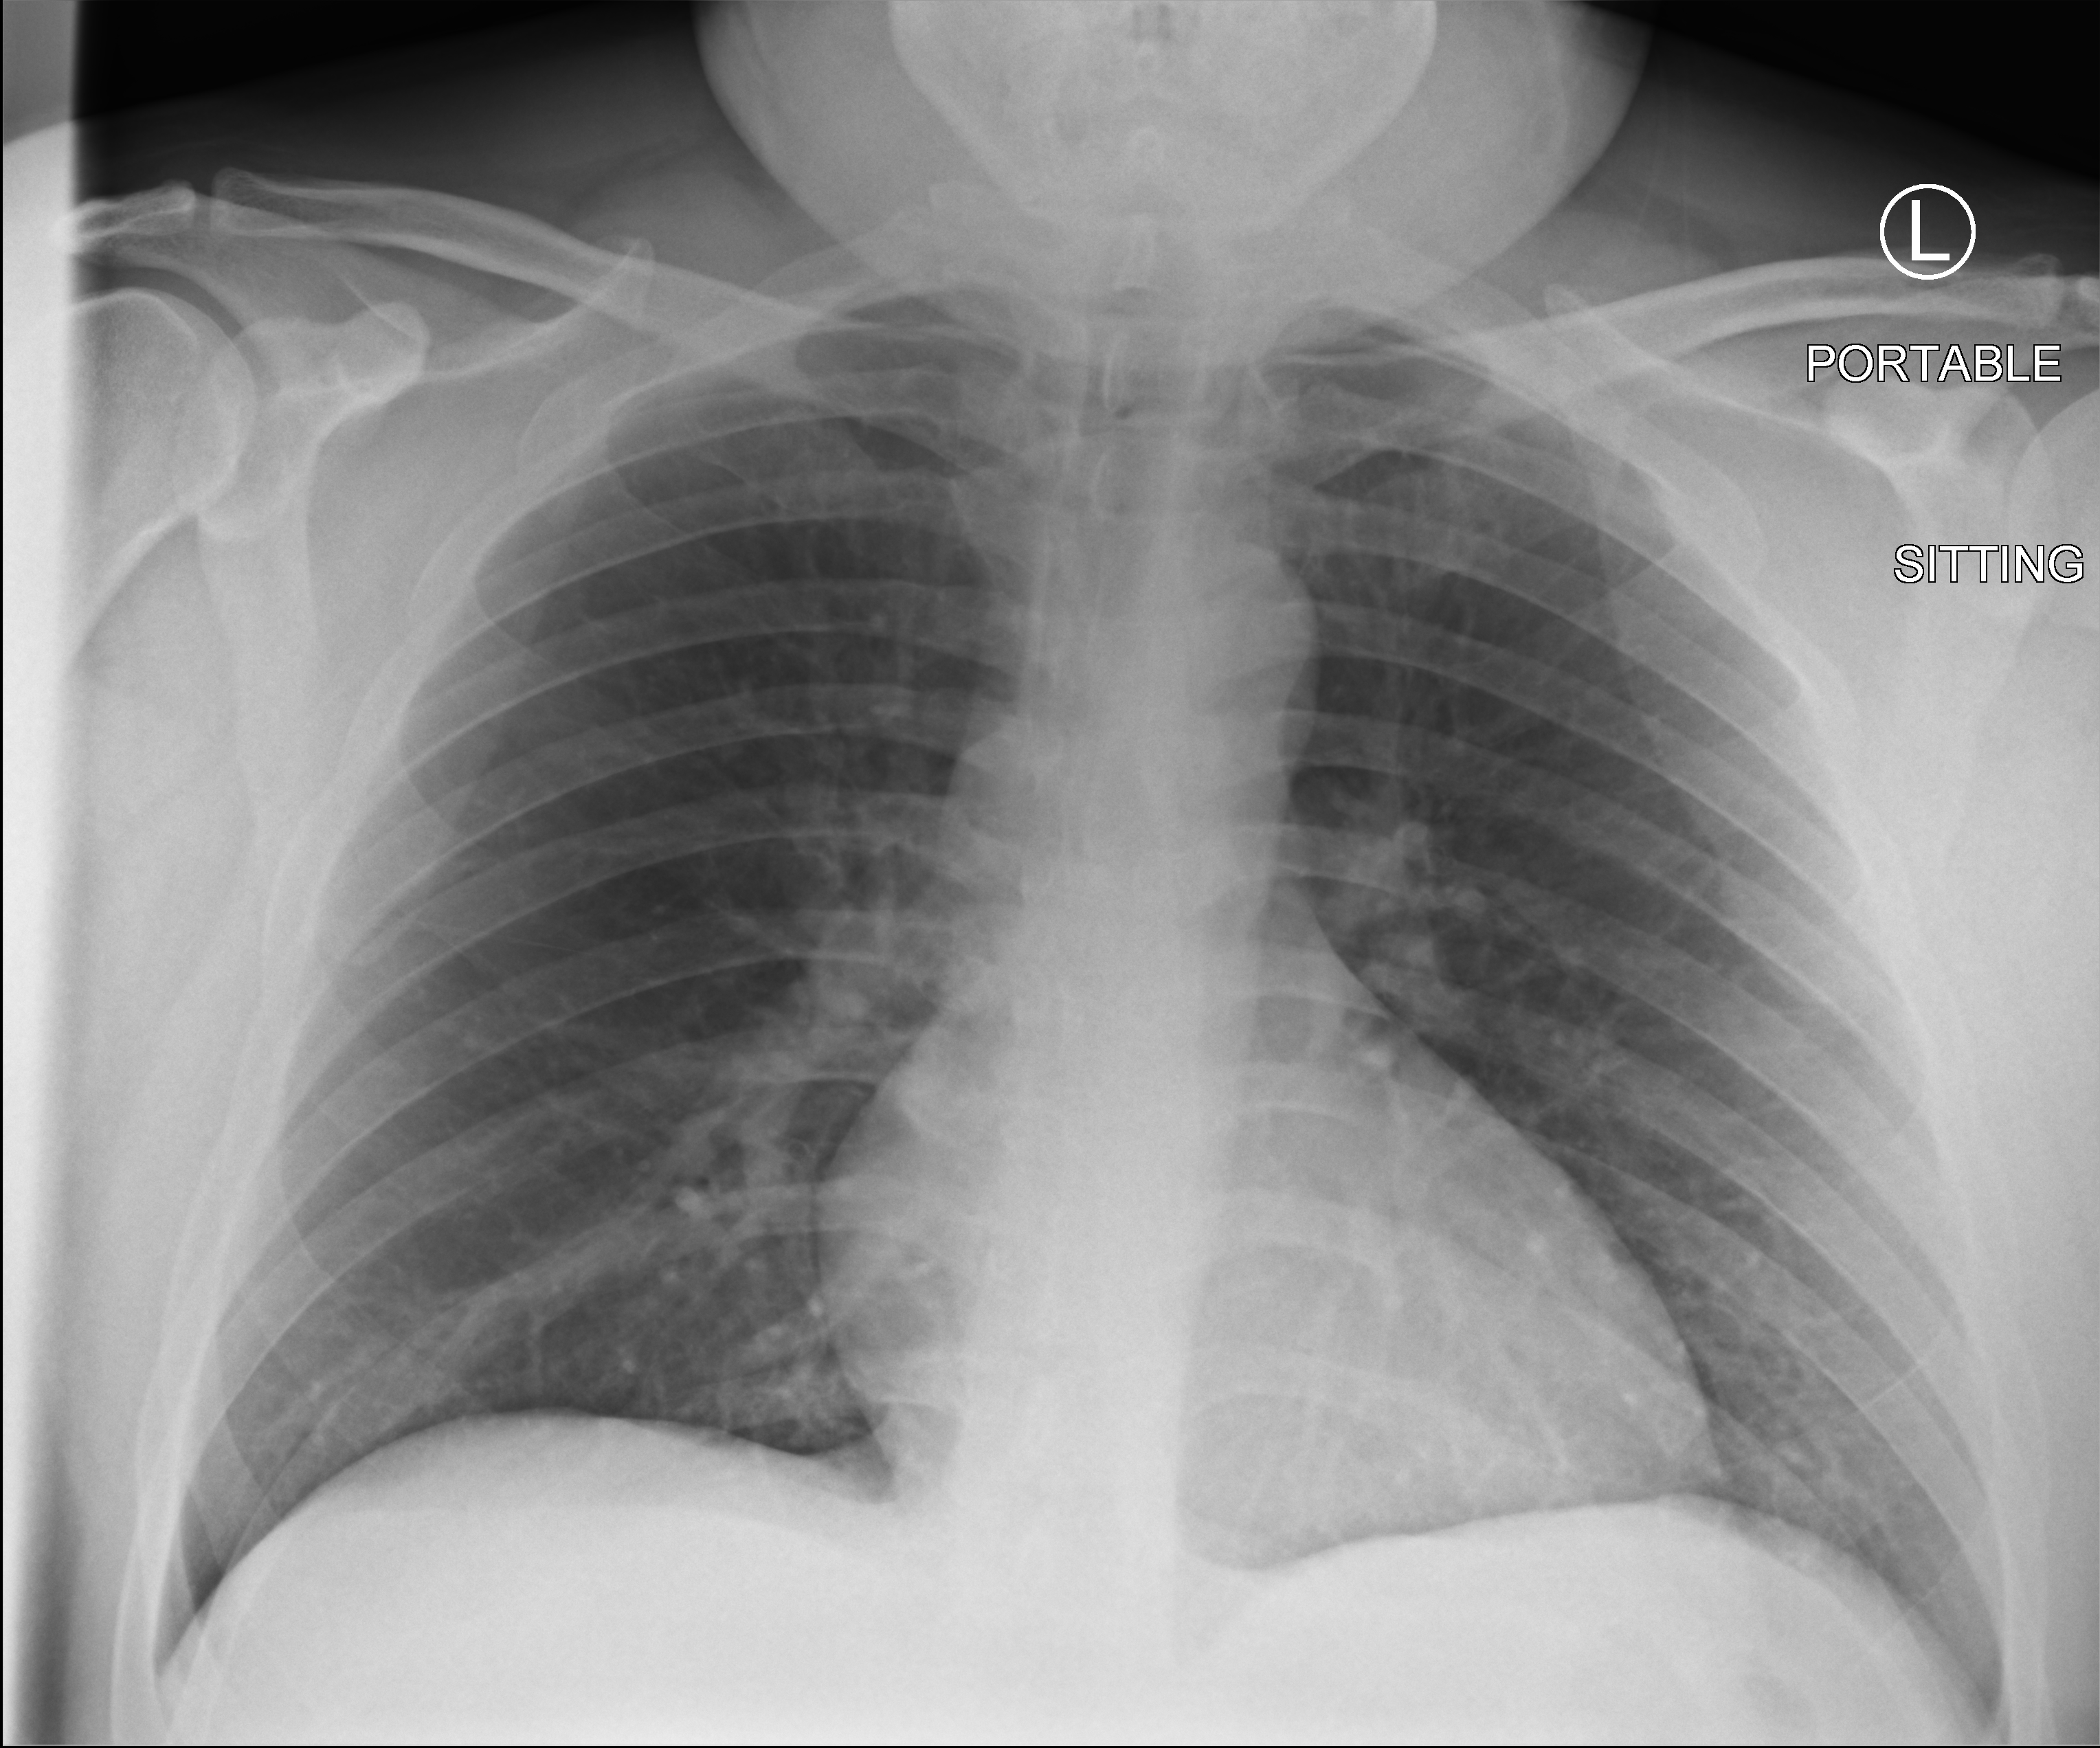
Chest X-ray (portable), anteroposterior (AP) projection. Patient hospitalised with COVID-19; male, aged 18–59 years.
Hospital-stay facts (about this admission, not read from this image; timing relative to this image not recorded): length of hospital stay: 1 day.